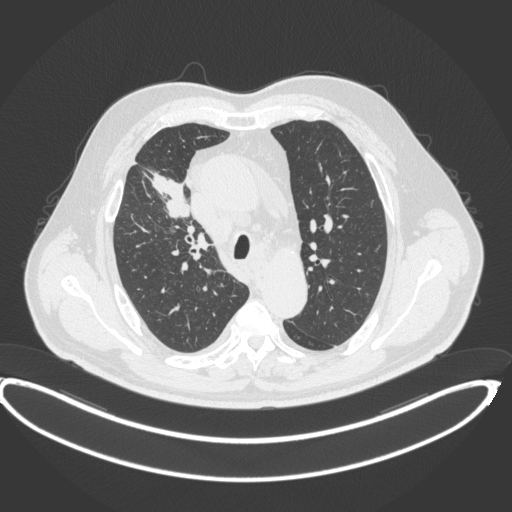
Chest CT, one axial slice. Position 288 of 395 along the scan axis. Lung window (W 1500 / L -600 HU). 1 mm slice thickness. 512 × 512 image matrix. Male patient, age 62 years. Case-level facts recorded for this patient, not image findings: clinical TNM (as recorded): T1c N3 M1c.
Structures marked on this image (rectangle marked by the reading radiologist):
- lung tumour (recorded histology: adenocarcinoma): bounding box [x1, y1, x2, y2] px = [144, 166, 193, 219]